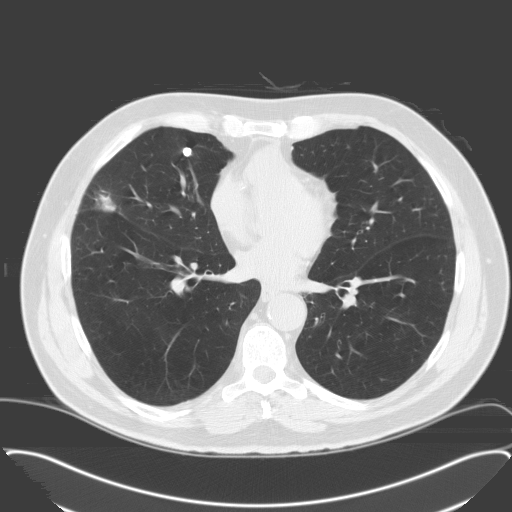
Chest CT (low-dose screening protocol), one axial image. Third screening round (two years after baseline). Lung window (W 1500 / L -600 HU). 3.2 mm slice thickness. 120 kVp. Male participant, aged 65 years at enrolment. Former smoker at enrolment.
Lesion marked by an expert reader, bounding box <63,168,131,228> (left, top, right, bottom; pixels). The exam's reader record, not a measurement of the box and not confirmed to be the same lesion: non-calcified nodule or mass ≥4 mm, right middle lobe, 28 × 23 mm, spiculated (stellate) margins, soft tissue attenuation, pre-existing on the prior screen: no. Official screen result: positive, other. Lung cancer was diagnosed 25 days after this screen: adenocarcinoma, NOS, right middle lobe, moderately differentiated (G2), stage IA (AJCC 6th edition), 25 mm at pathology.